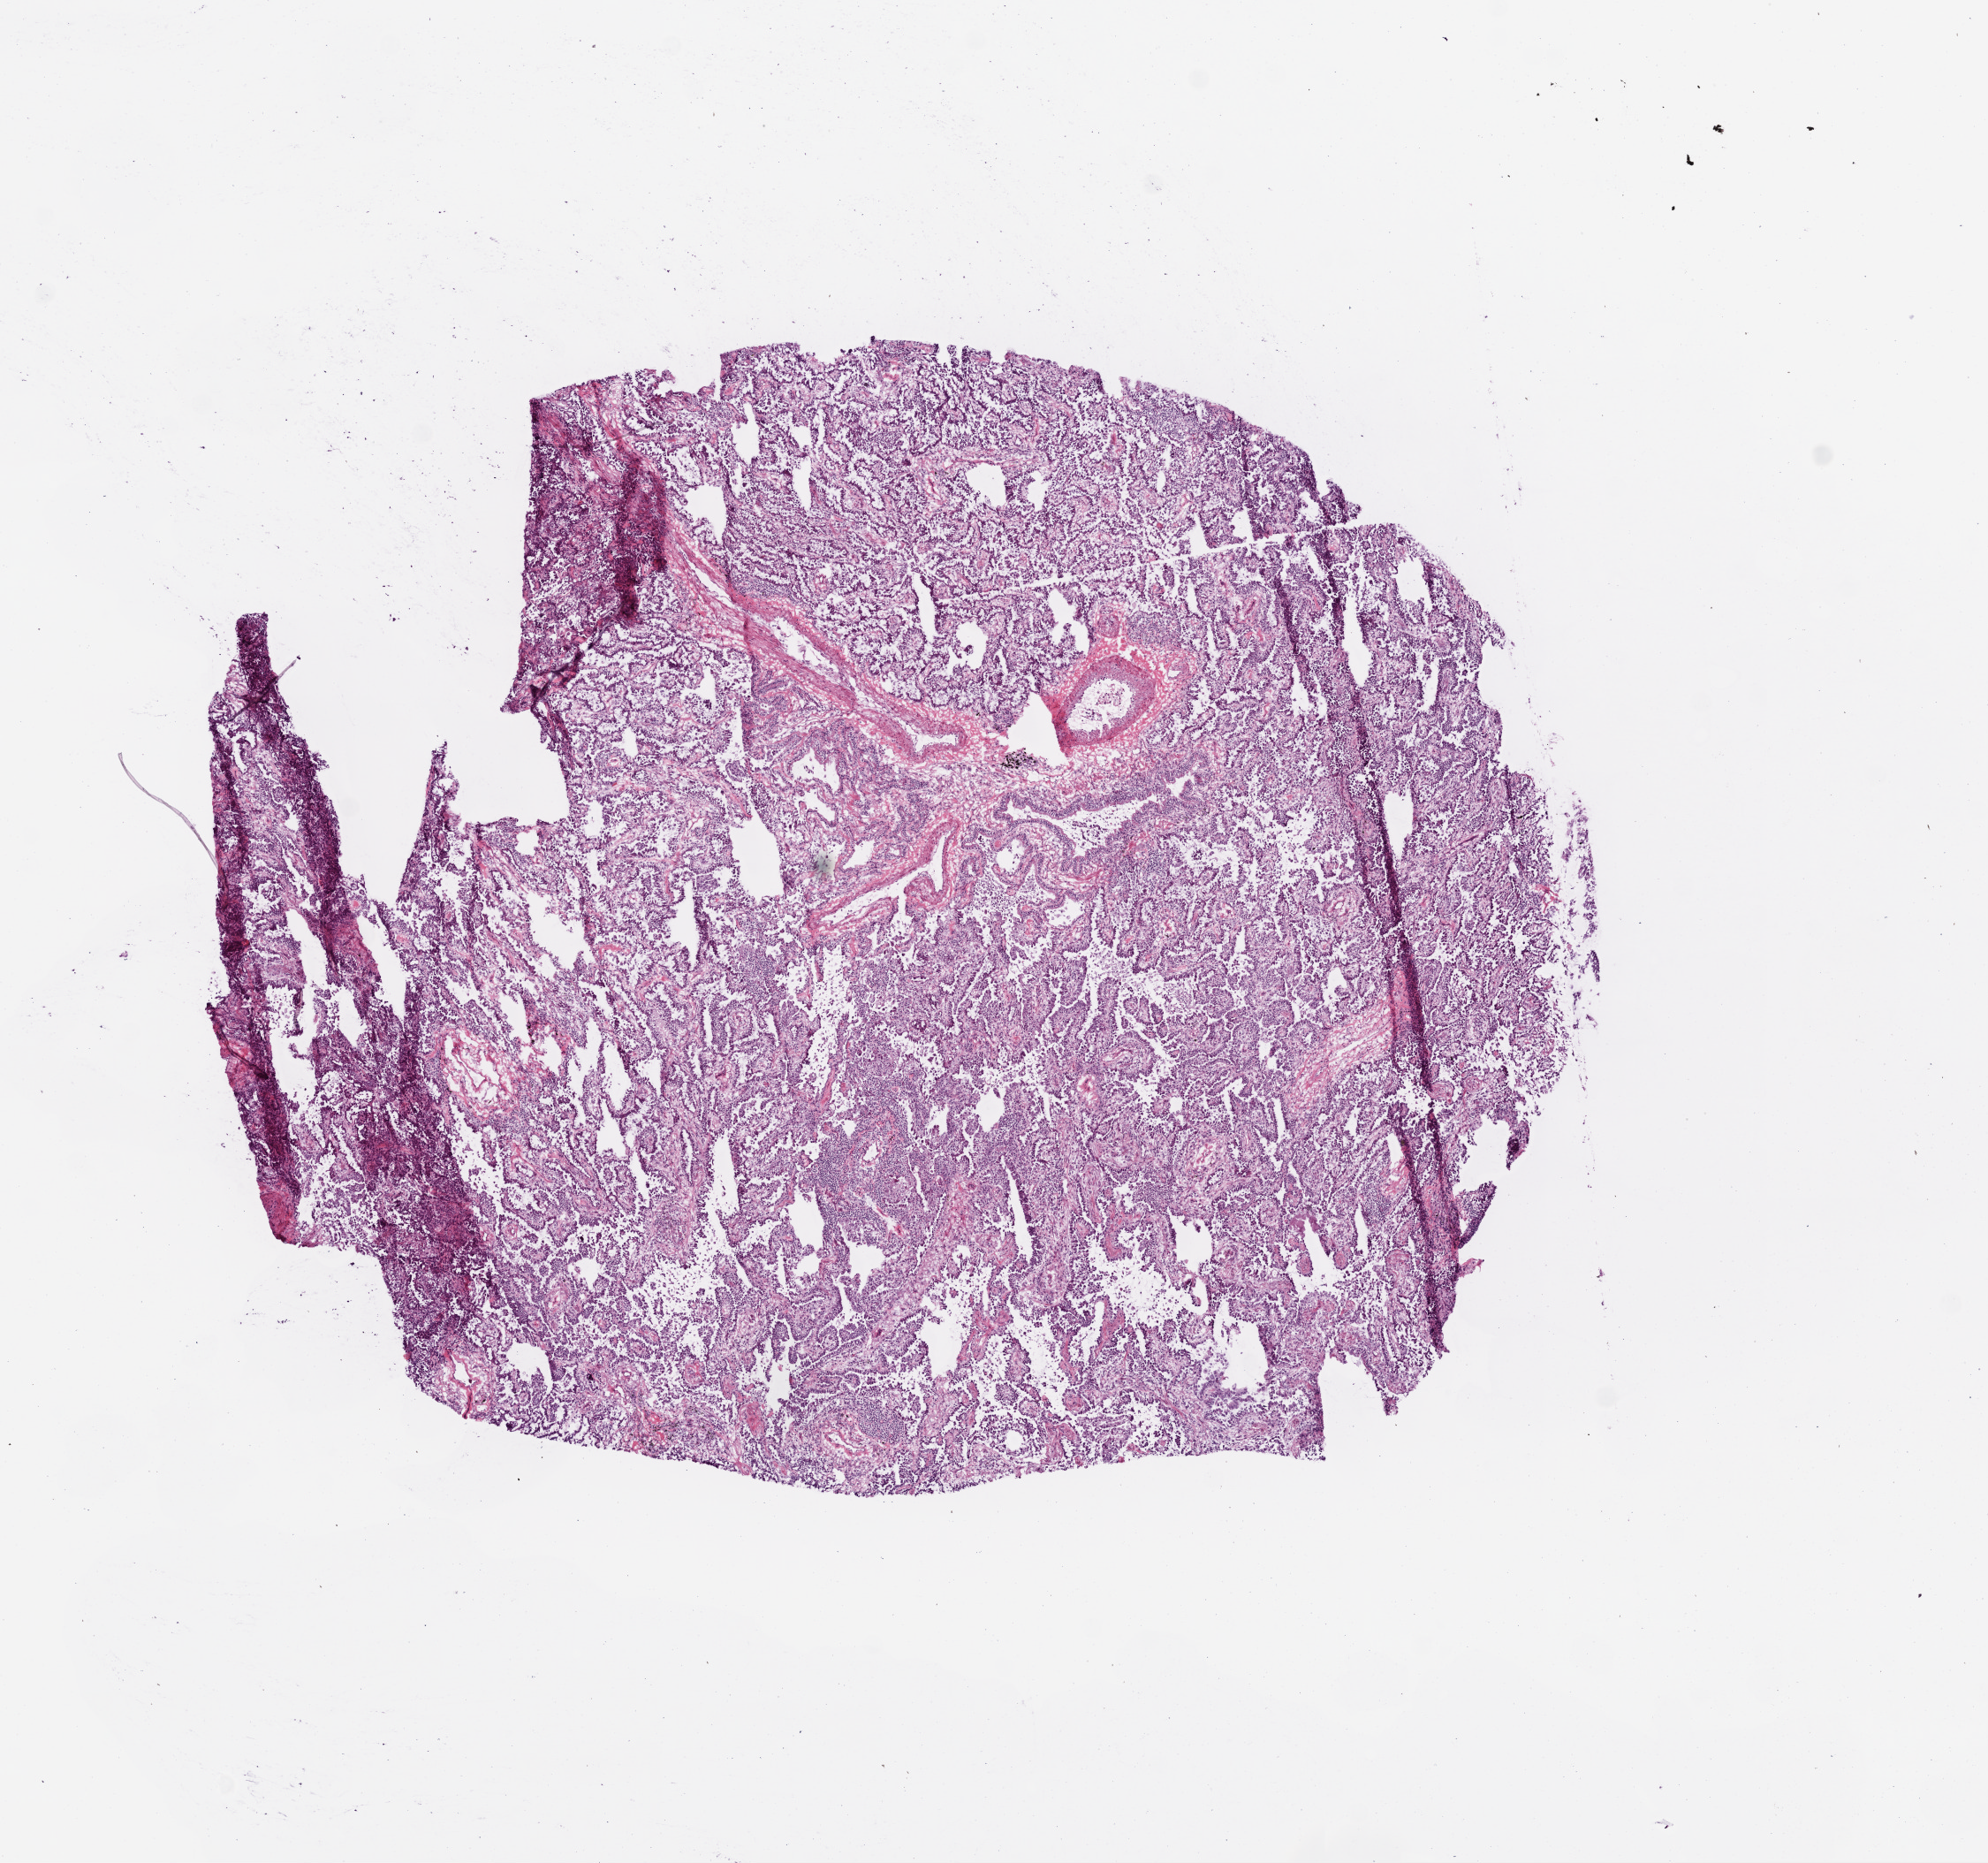
H&E whole-slide image, a low-resolution overview of the entire scanned area, about 9.0 x 8.5 mm; frozen section from the top of the tissue portion; sample: primary tumour, lung. Patient: male, age at initial diagnosis 67 years. Composition of this section per pathologist review: tumour cells 80%, tumour nuclei 80%, normal cells 0%, stromal cells 20%, necrosis 0%.
Diagnosis: Adenocarcinoma, NOS (lower lobe, lung). AJCC pathologic stage: IB (6th edition).